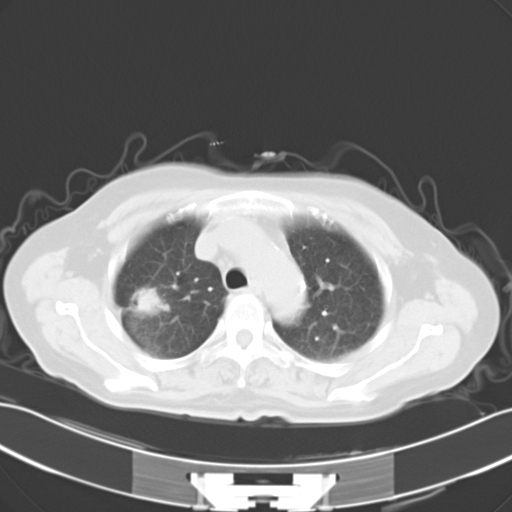
Chest CT, one axial slice. Position 22 of 28 along the scan axis. Lung window (W 1500 / L -600 HU). 512 × 512 image matrix. Patient: female, 65 years. Case-level facts recorded for this patient, not image findings: clinical TNM (as recorded): T1c N0 M1c.
Structures marked on this image (bounding box drawn by a radiologist):
- lung tumour (recorded histology: adenocarcinoma): bounding box (x1, y1, x2, y2) in pixels: (136, 284, 157, 314)